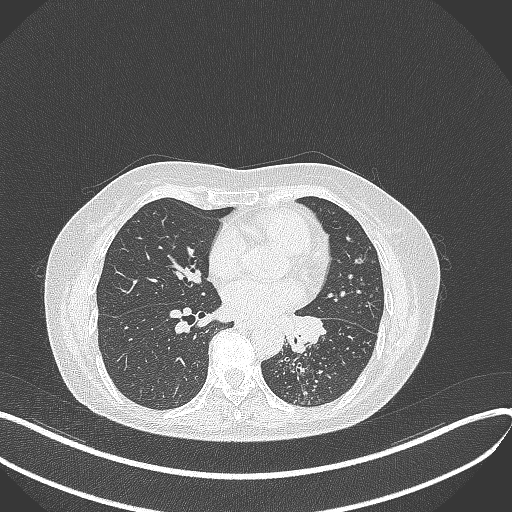
Chest CT, one axial slice; lung window (W 1500 / L -600 HU); 1 mm slice thickness; 512 × 512 image matrix. Female patient, age 63 years. From the clinical record (not read from this slice): clinical TNM (as recorded): T1b N0 M0; histopathological grade: G2-3.
Structures marked on this image (rectangle marked by the reading radiologist):
- lung tumour (recorded histology: adenocarcinoma): bounding box [x1, y1, x2, y2] px = [282, 310, 330, 355]